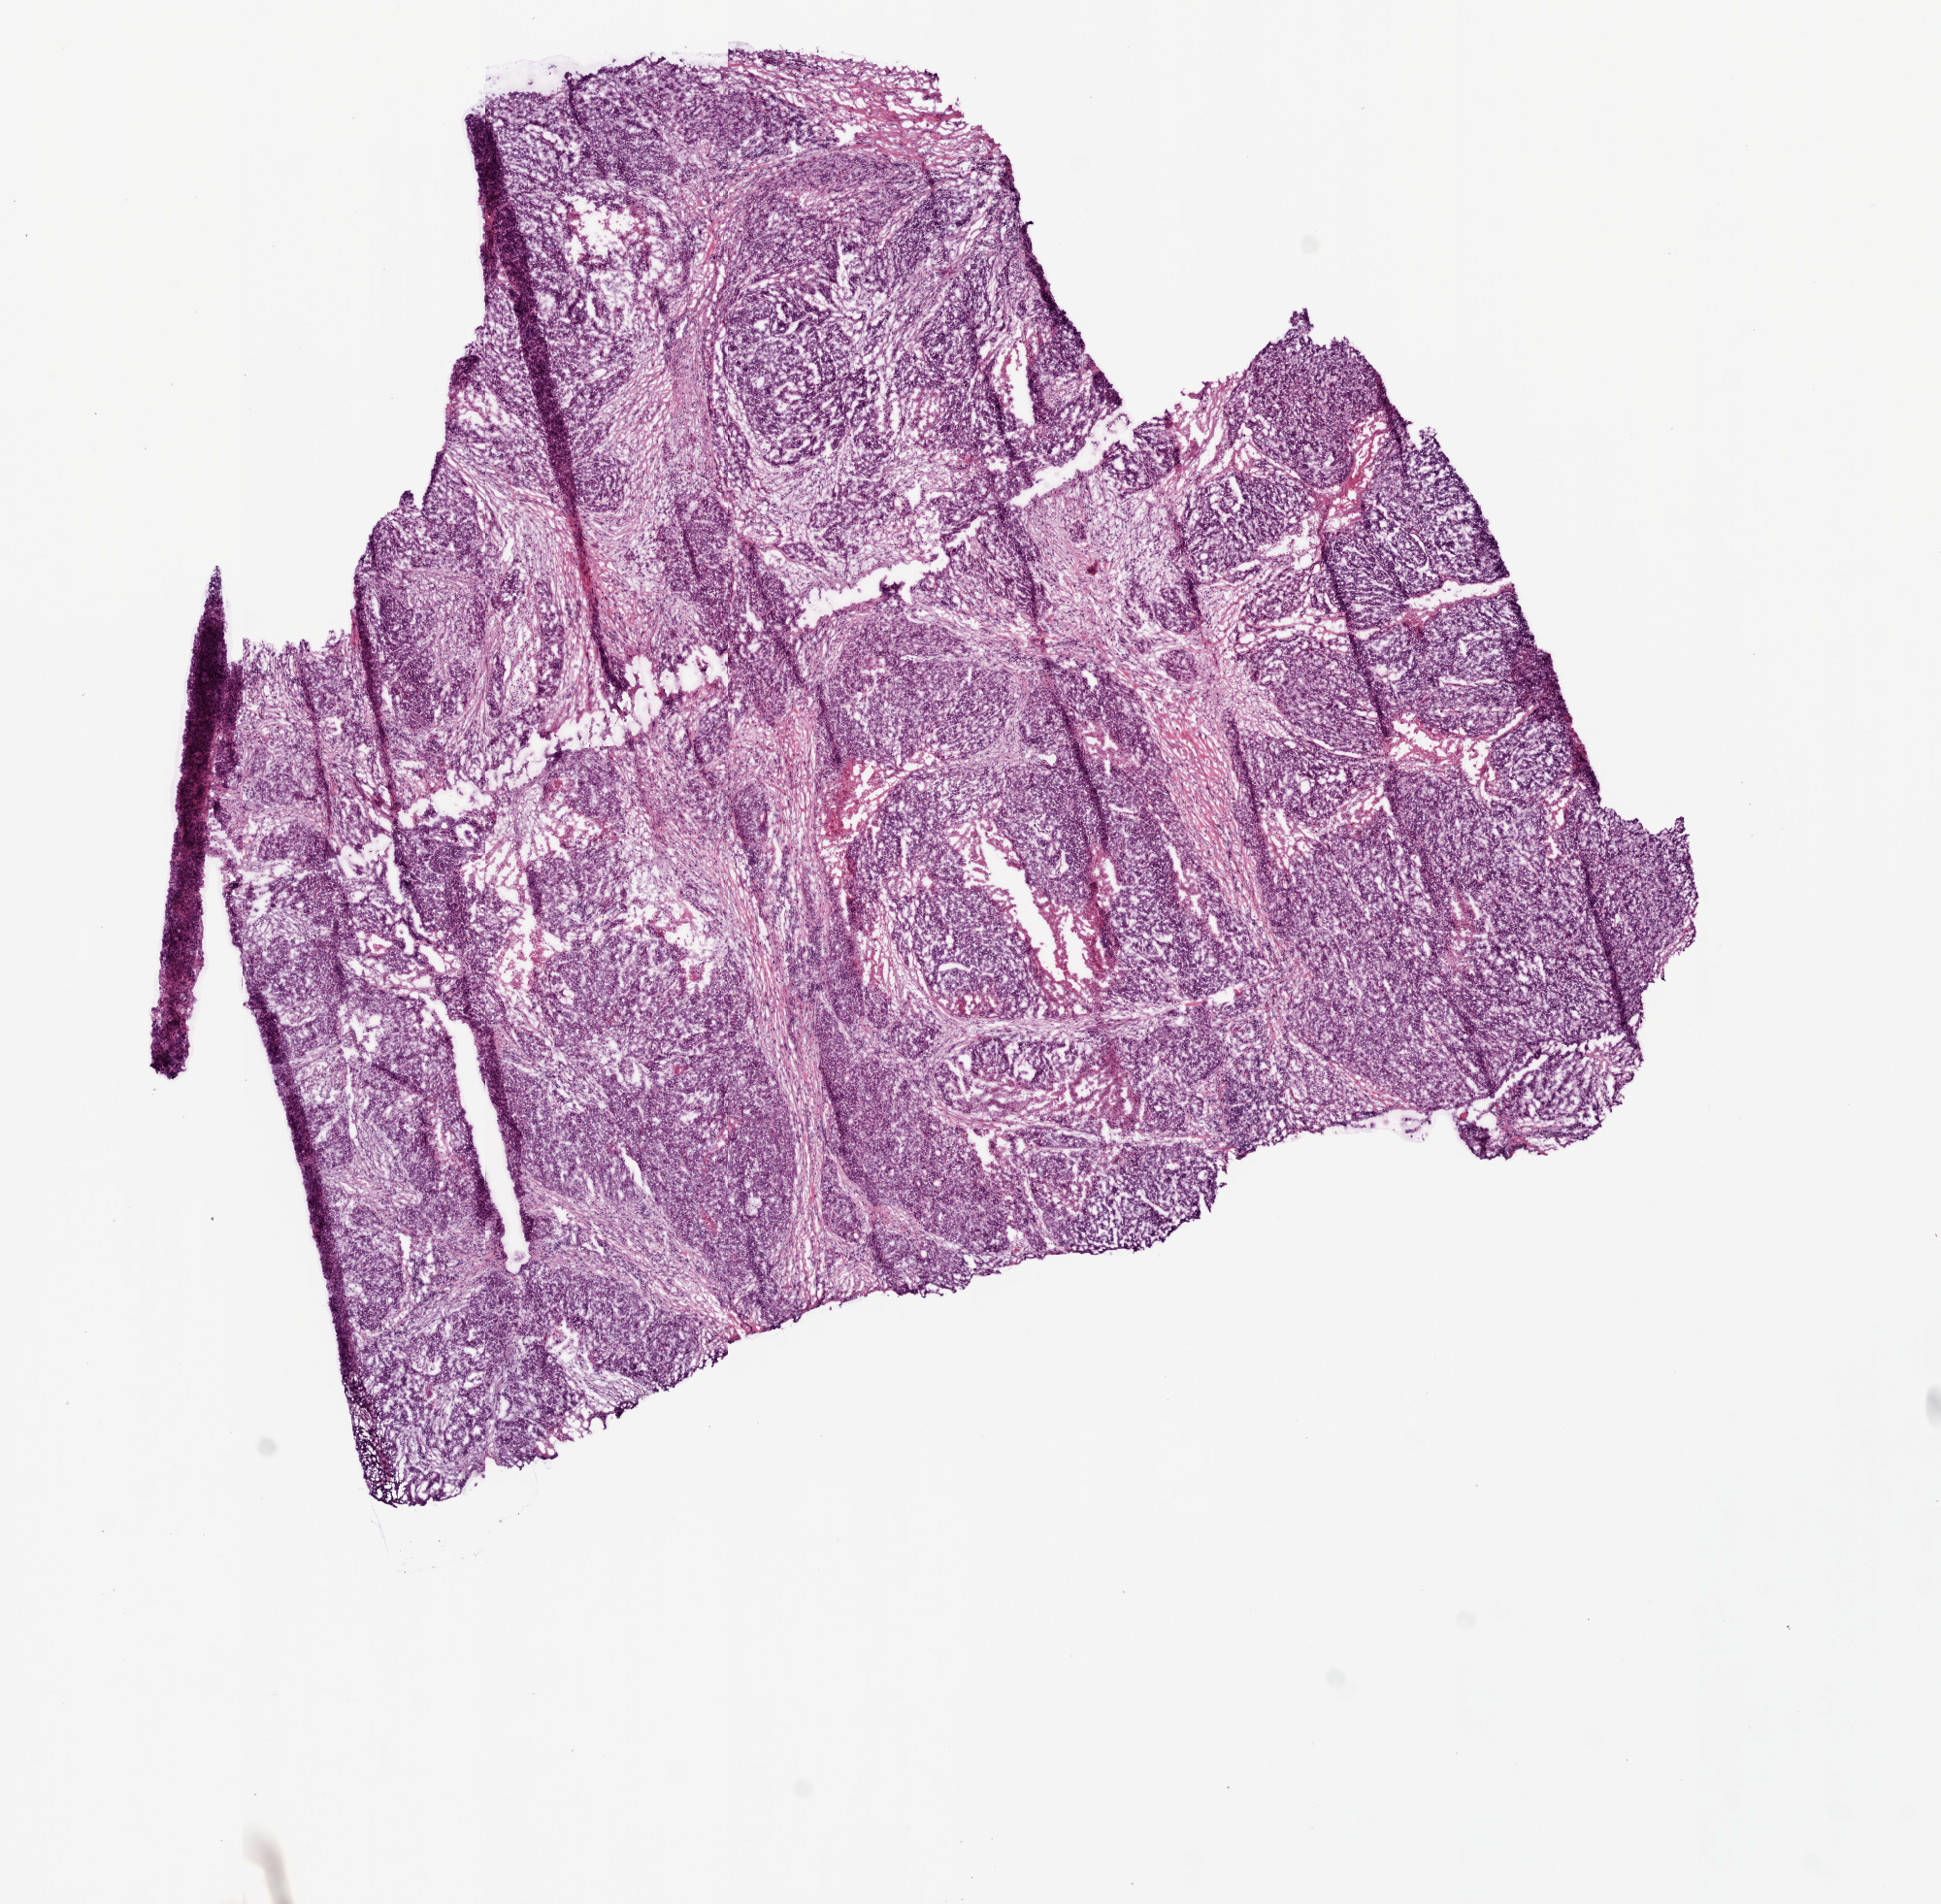
Digitized H&E tissue section (whole slide), shown as a low-resolution overview of the whole scanned area (about 8.0 x 7.9 mm); frozen section; sample: primary tumour, head and neck. Male patient; age at initial diagnosis 52 years. Histologic grade: G3 (poorly differentiated). Composition of this section per pathologist review: tumour cells 80%, tumour nuclei 80%, normal cells 0%, stromal cells 15%, necrosis 5%.
AJCC pathologic stage: IVA (7th edition). Laterality: left. Pathologic diagnosis: Squamous cell carcinoma, NOS. Lymph nodes positive (case pathology): 5 of 70 examined.